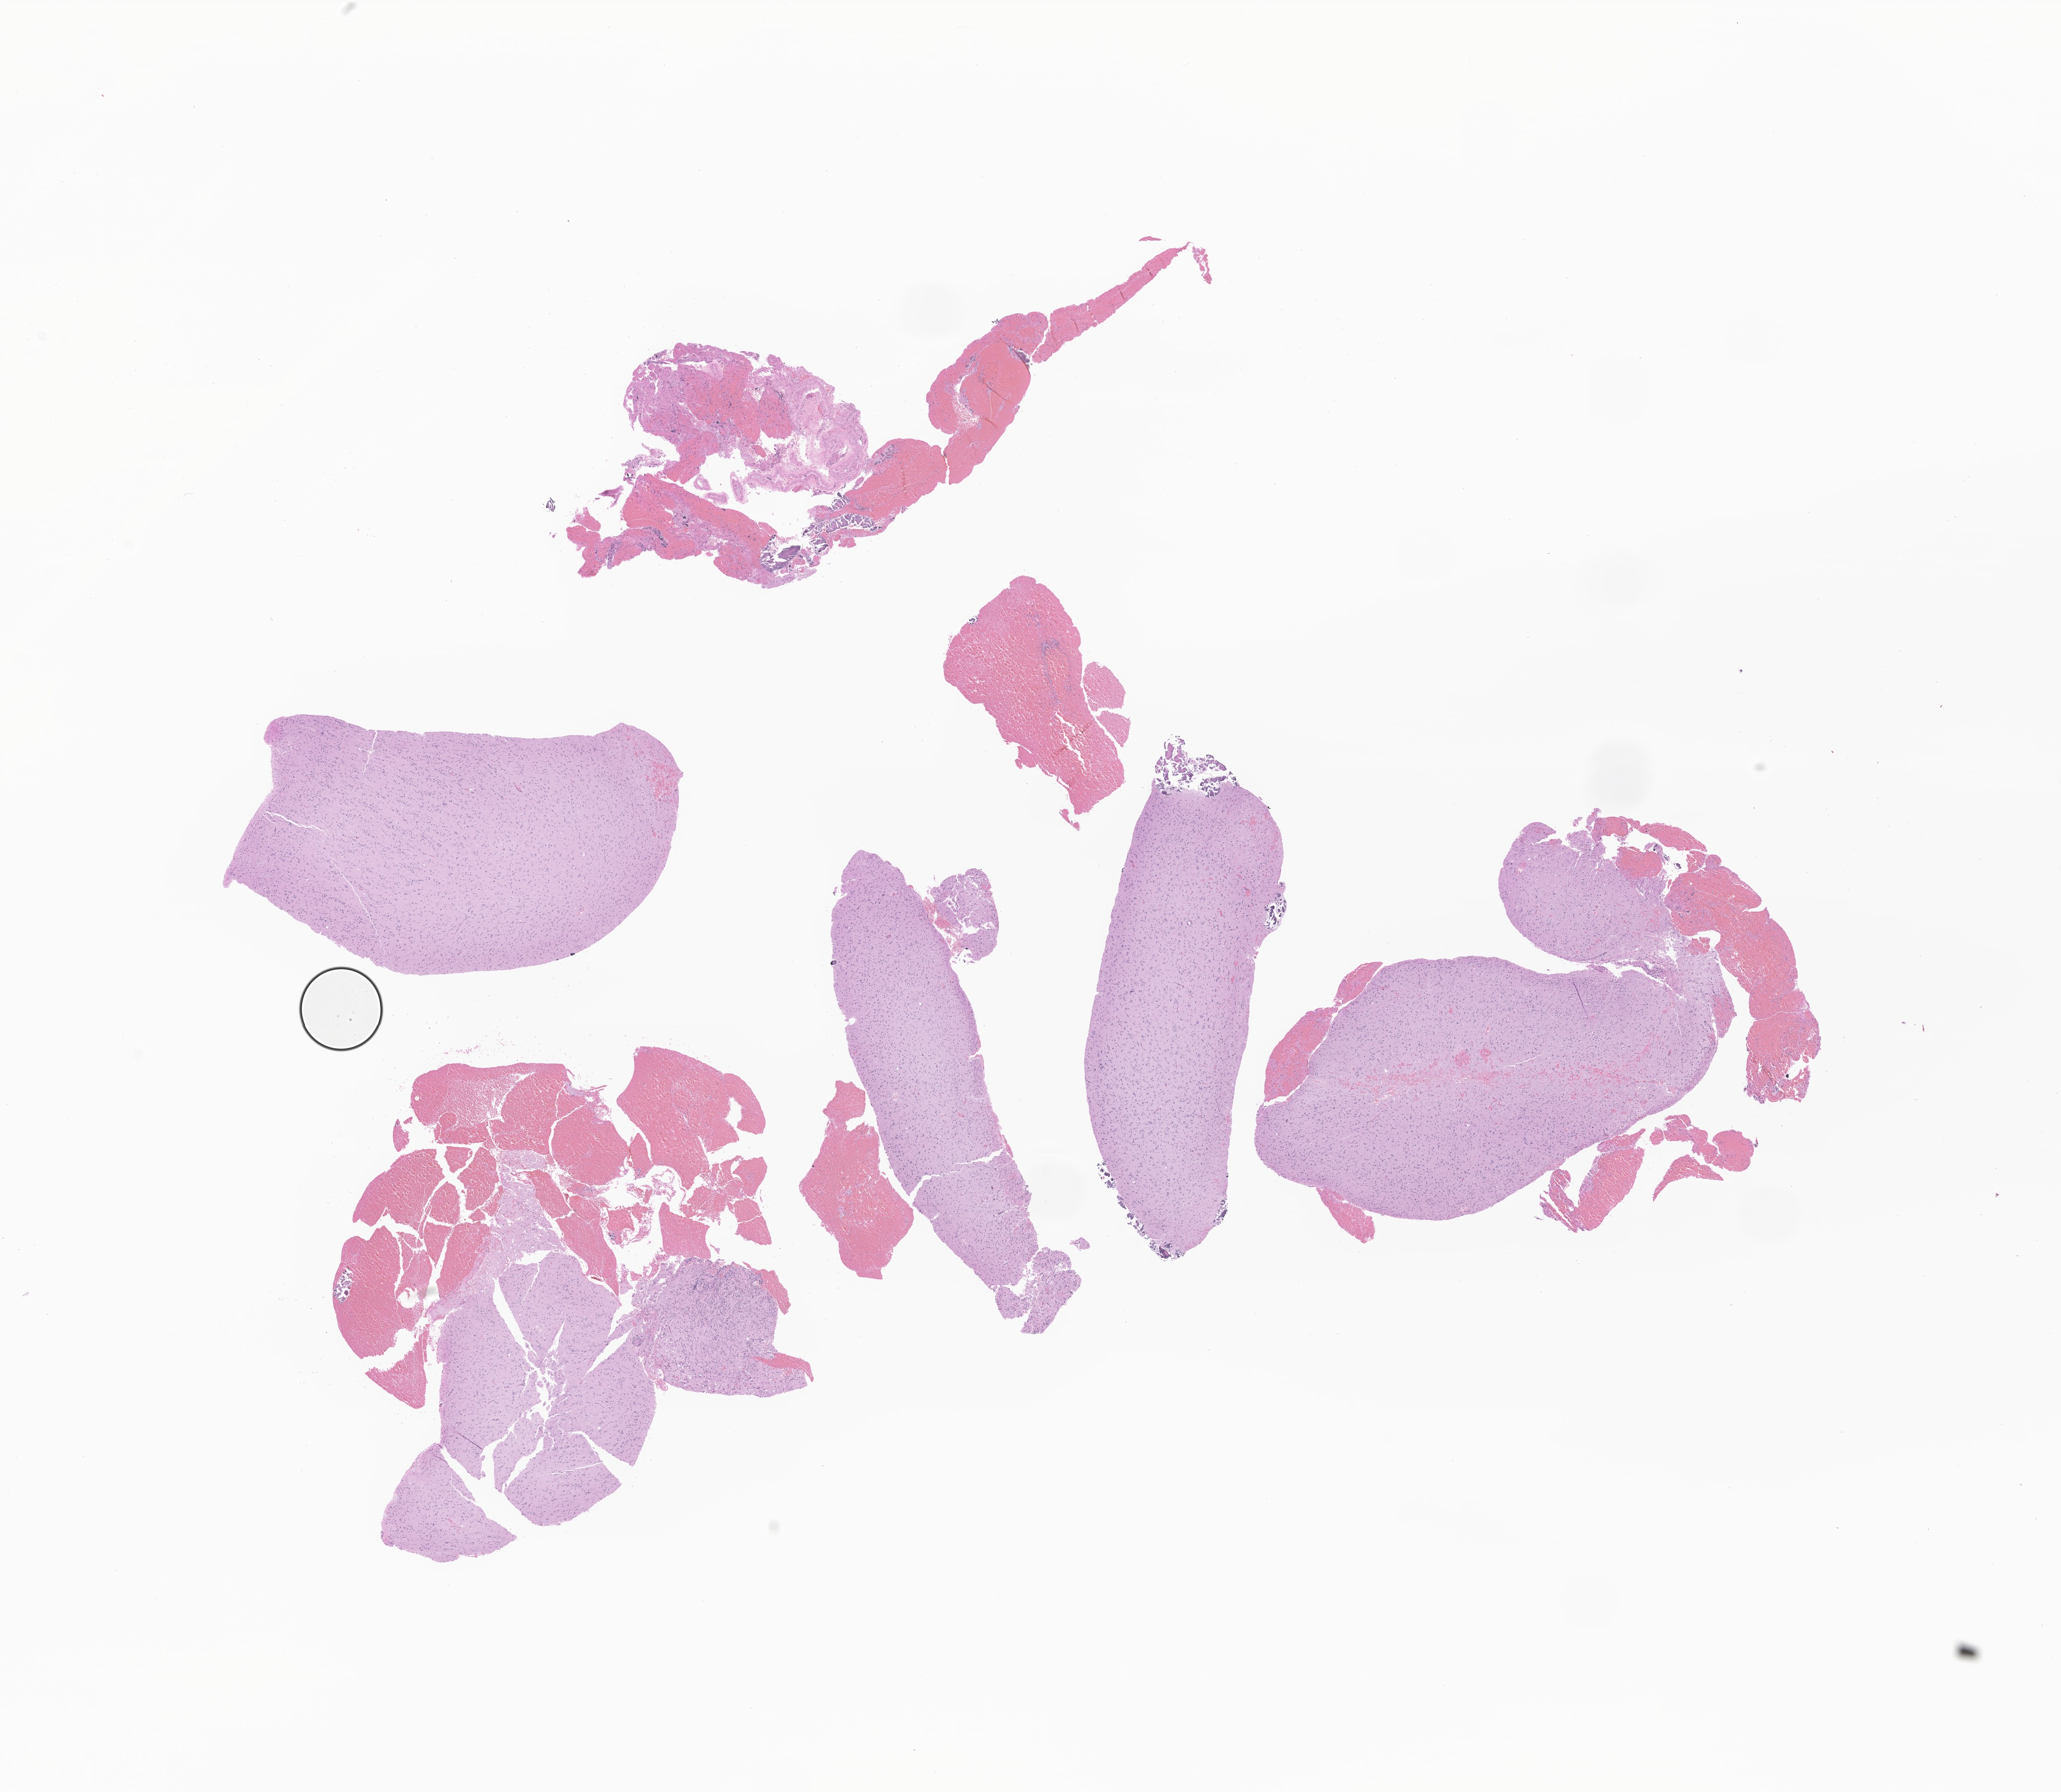
Haematoxylin and eosin whole-slide image of tumor tissue from the occipital lobe — a low-resolution overview of the entire scanned area, about 17.2 x 15.0 mm, formalin-fixed, paraffin-embedded (FFPE) tissue. Male patient, age 223 months (18 years 7 months).
Diagnosis (ICD-O-3 morphology term): Glioma, malignant.